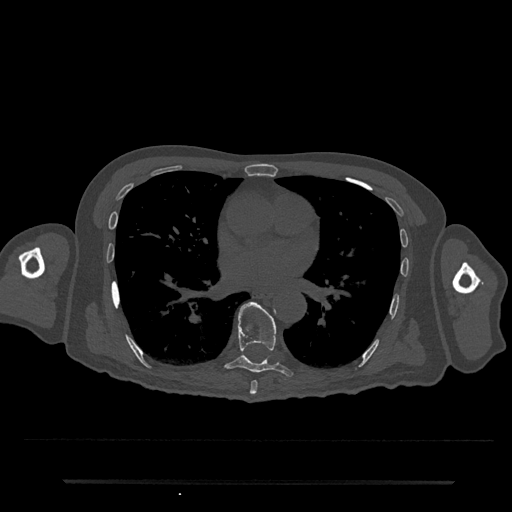
CT including the spine, one axial slice. Slice 428 of 797 in the series (ordered by position). Reconstruction kernel Br40s/3. 120 kVp. Bone window (W 1800 / L 400 HU). 512 × 512 image matrix, field of view 427 × 427 mm. Patient: male, 74 years. From the clinical record (not read from this slice): primary cancer: prostate.
Structures marked on this image (semi-automatic segmentation, software-assisted and operator-edited):
- T7 vertebra: bounding box (x1, y1, x2, y2) in pixels: (250, 380, 258, 395)
- T8 vertebra: (225, 302, 293, 377)